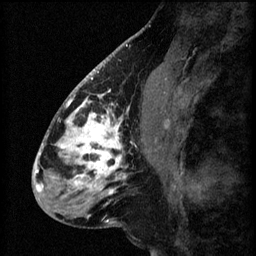
Breast MRI (dynamic contrast-enhanced), one sagittal slice; slice 28 of 60 in the series (ordered by position); 3 images stored at this slice position (order not interpretable as contrast timing); 1.5 T; TE 4.2 ms, TR 8.2 ms; 256 × 256 image matrix, field of view 180 × 180 mm. Female patient, age 41 years.
Annotated regions visible in this slice (semi-automatic segmentation, software-assisted and operator-edited):
- analysis volume of interest (the breast-tissue region the enhancement analysis was run in; not a lesion): box from (x=56, y=104) to (x=157, y=207) px
- tumour enhancement mask (voxels above the 70 % enhancement threshold inside the analysis volume of interest): (x=58, y=104)–(x=135, y=195)